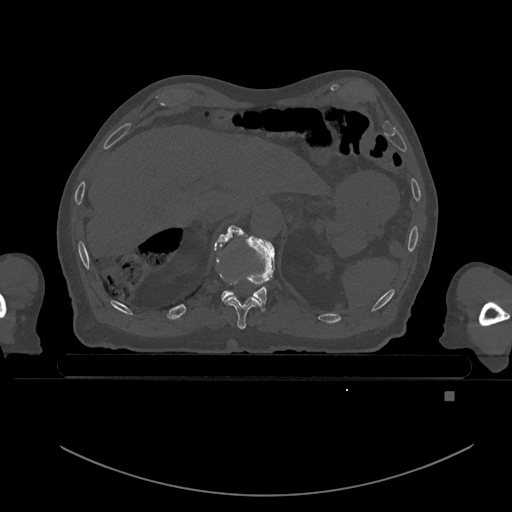
CT including the spine, one axial slice. Slice 60 of 969 in the series (ordered by position). Bone window (W 1800 / L 400 HU). 512 × 512 image matrix, field of view 456 × 456 mm. Patient: male, 82 years. From the clinical record (not read from this slice): primary cancer: prostate; vertebrae with lytic lesions (as recorded): T11, T9, T8, T2.
Annotated regions visible in this slice (semi-automatic segmentation, software-assisted and operator-edited):
- T10 vertebra: bounding box [x1, y1, x2, y2] px = [214, 241, 260, 330]
- T11 vertebra: [218, 224, 275, 311]